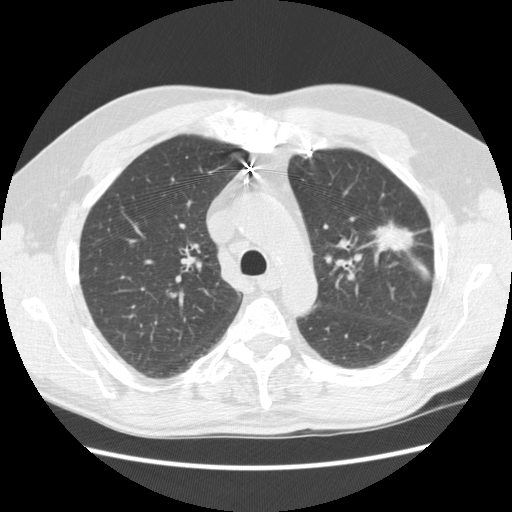
Low-dose screening chest CT, one axial slice. Slice 169 of 231 in the series (ordered by position). Reconstruction kernel STANDARD. 120 kVp. Lung window (W 1500 / L -600 HU). 2.5 mm slice thickness. 512 × 512 image matrix.
Annotated regions visible in this slice (expert manual segmentation):
- lesion 1 (tumor, upper lobe of left lung): box from (x=372, y=221) to (x=415, y=253) px